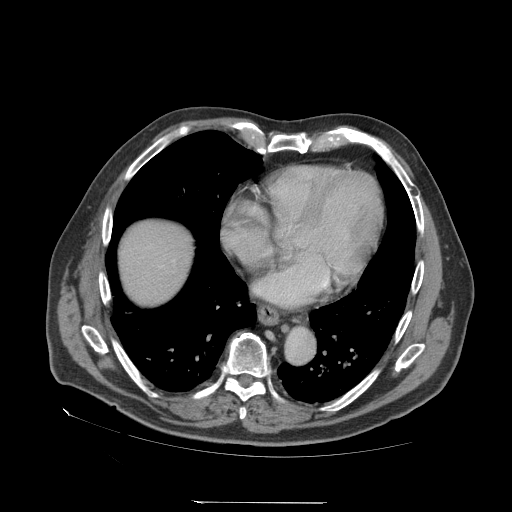
Contrast-enhanced abdominal CT (liver protocol), one axial slice. Position 72 of 83 along the scan axis. Reconstruction kernel STANDARD. 140 kVp. Soft-tissue window (W 400 / L 40 HU). 512 × 512 image matrix. Case-level facts recorded for this patient, not image findings: diagnosis: hepatocellular carcinoma (patient treated with transarterial chemoembolisation; whether this scan precedes or follows treatment is not stated here); TNM stage (as recorded): Stage-I; Child-Pugh class: A; tumour differentiation: well differentiated.
Structures marked on this image (semi-automatic segmentation, software-assisted and operator-edited):
- liver parenchyma outside the tumour (the mass and vessels are separate outlines, so this box may not span the whole liver): bounding box [x1, y1, x2, y2] px = [120, 220, 192, 304]